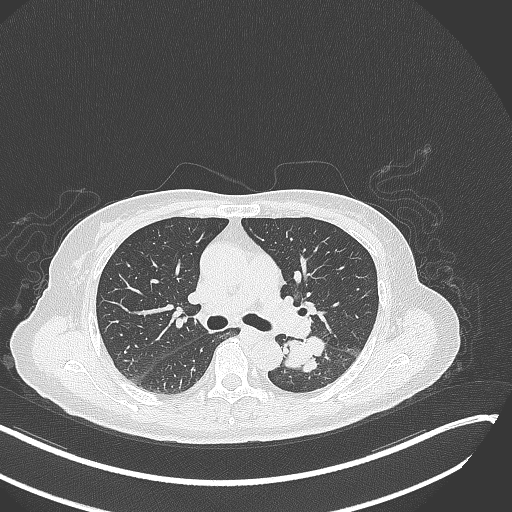
Chest CT, one axial slice; reconstruction kernel B70f; 120 kVp; lung window (W 1500 / L -600 HU); 512 × 512 image matrix, field of view 400 × 400 mm. Female patient, age 64 years. Case-level facts recorded for this patient, not image findings: clinical TNM (as recorded): T3 N1 M1; histopathological grade: G3.
Outlined on this slice (bounding box drawn by a radiologist):
- lung tumour (recorded histology: small cell carcinoma): bounding box (x1, y1, x2, y2) in pixels: (284, 336, 330, 379)